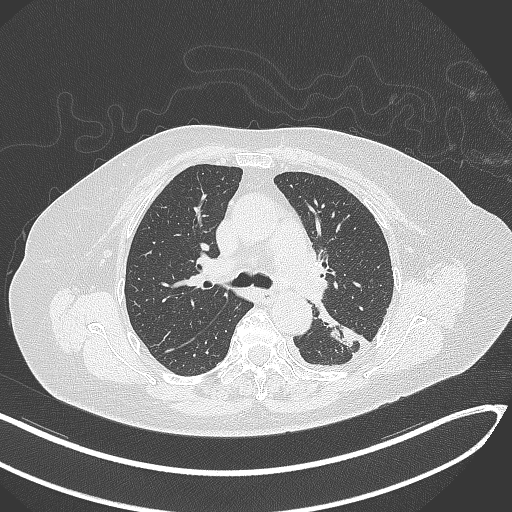
Chest CT, one axial slice; slice 204 of 270 in the series (ordered by position); reconstruction kernel B70f; 120 kVp; lung window (W 1500 / L -600 HU); 1 mm slice thickness; 512 × 512 image matrix. Patient: female, 76 years. Case-level facts recorded for this patient, not image findings: clinical TNM (as recorded): T1c N0 M0.
Annotated regions visible in this slice (bounding box drawn by a radiologist):
- lung tumour (recorded histology: adenocarcinoma): box from (x=317, y=310) to (x=364, y=350) px